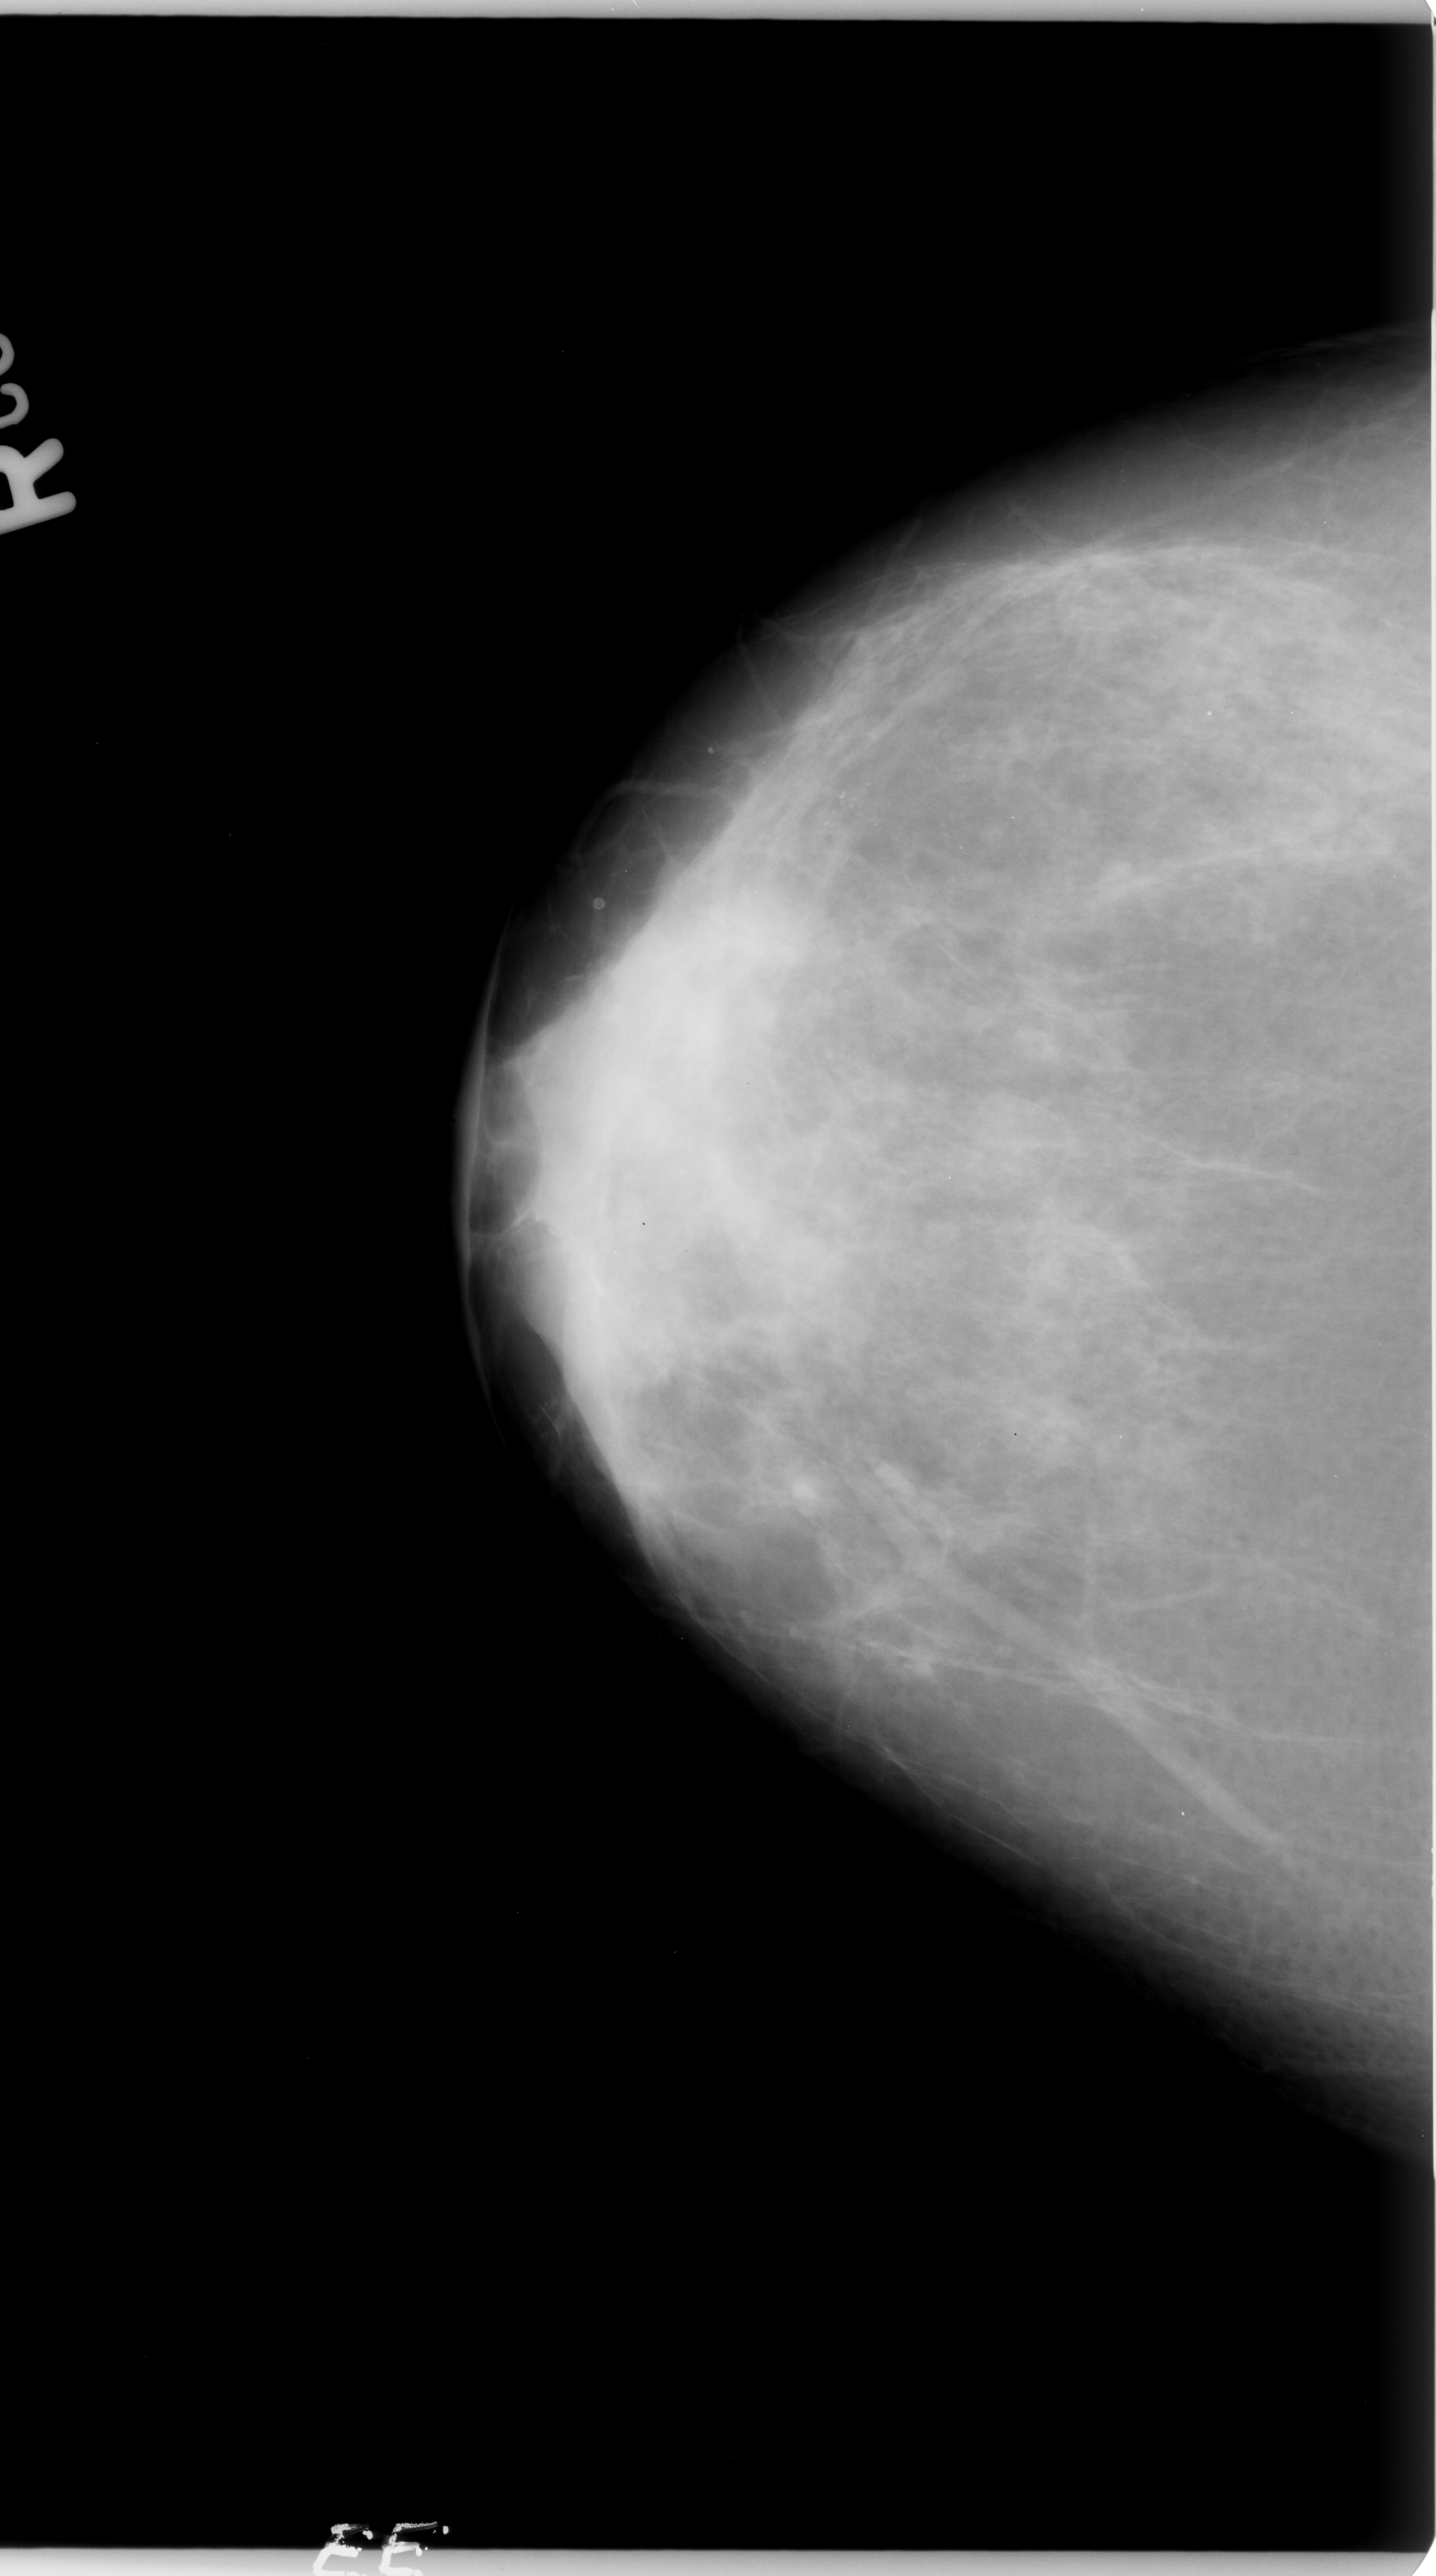
Scanned film-screen mammogram; right breast; craniocaudal (CC) view; 1436 × 2576 image matrix.
Marked abnormalities (boxes around the expert regions of interest):
- calcifications, morphology pleomorphic, distribution segmental; BI-RADS assessment category 4; pathology (as recorded): benign: bounding box <666,808,1014,1014> (left, top, right, bottom; pixels)